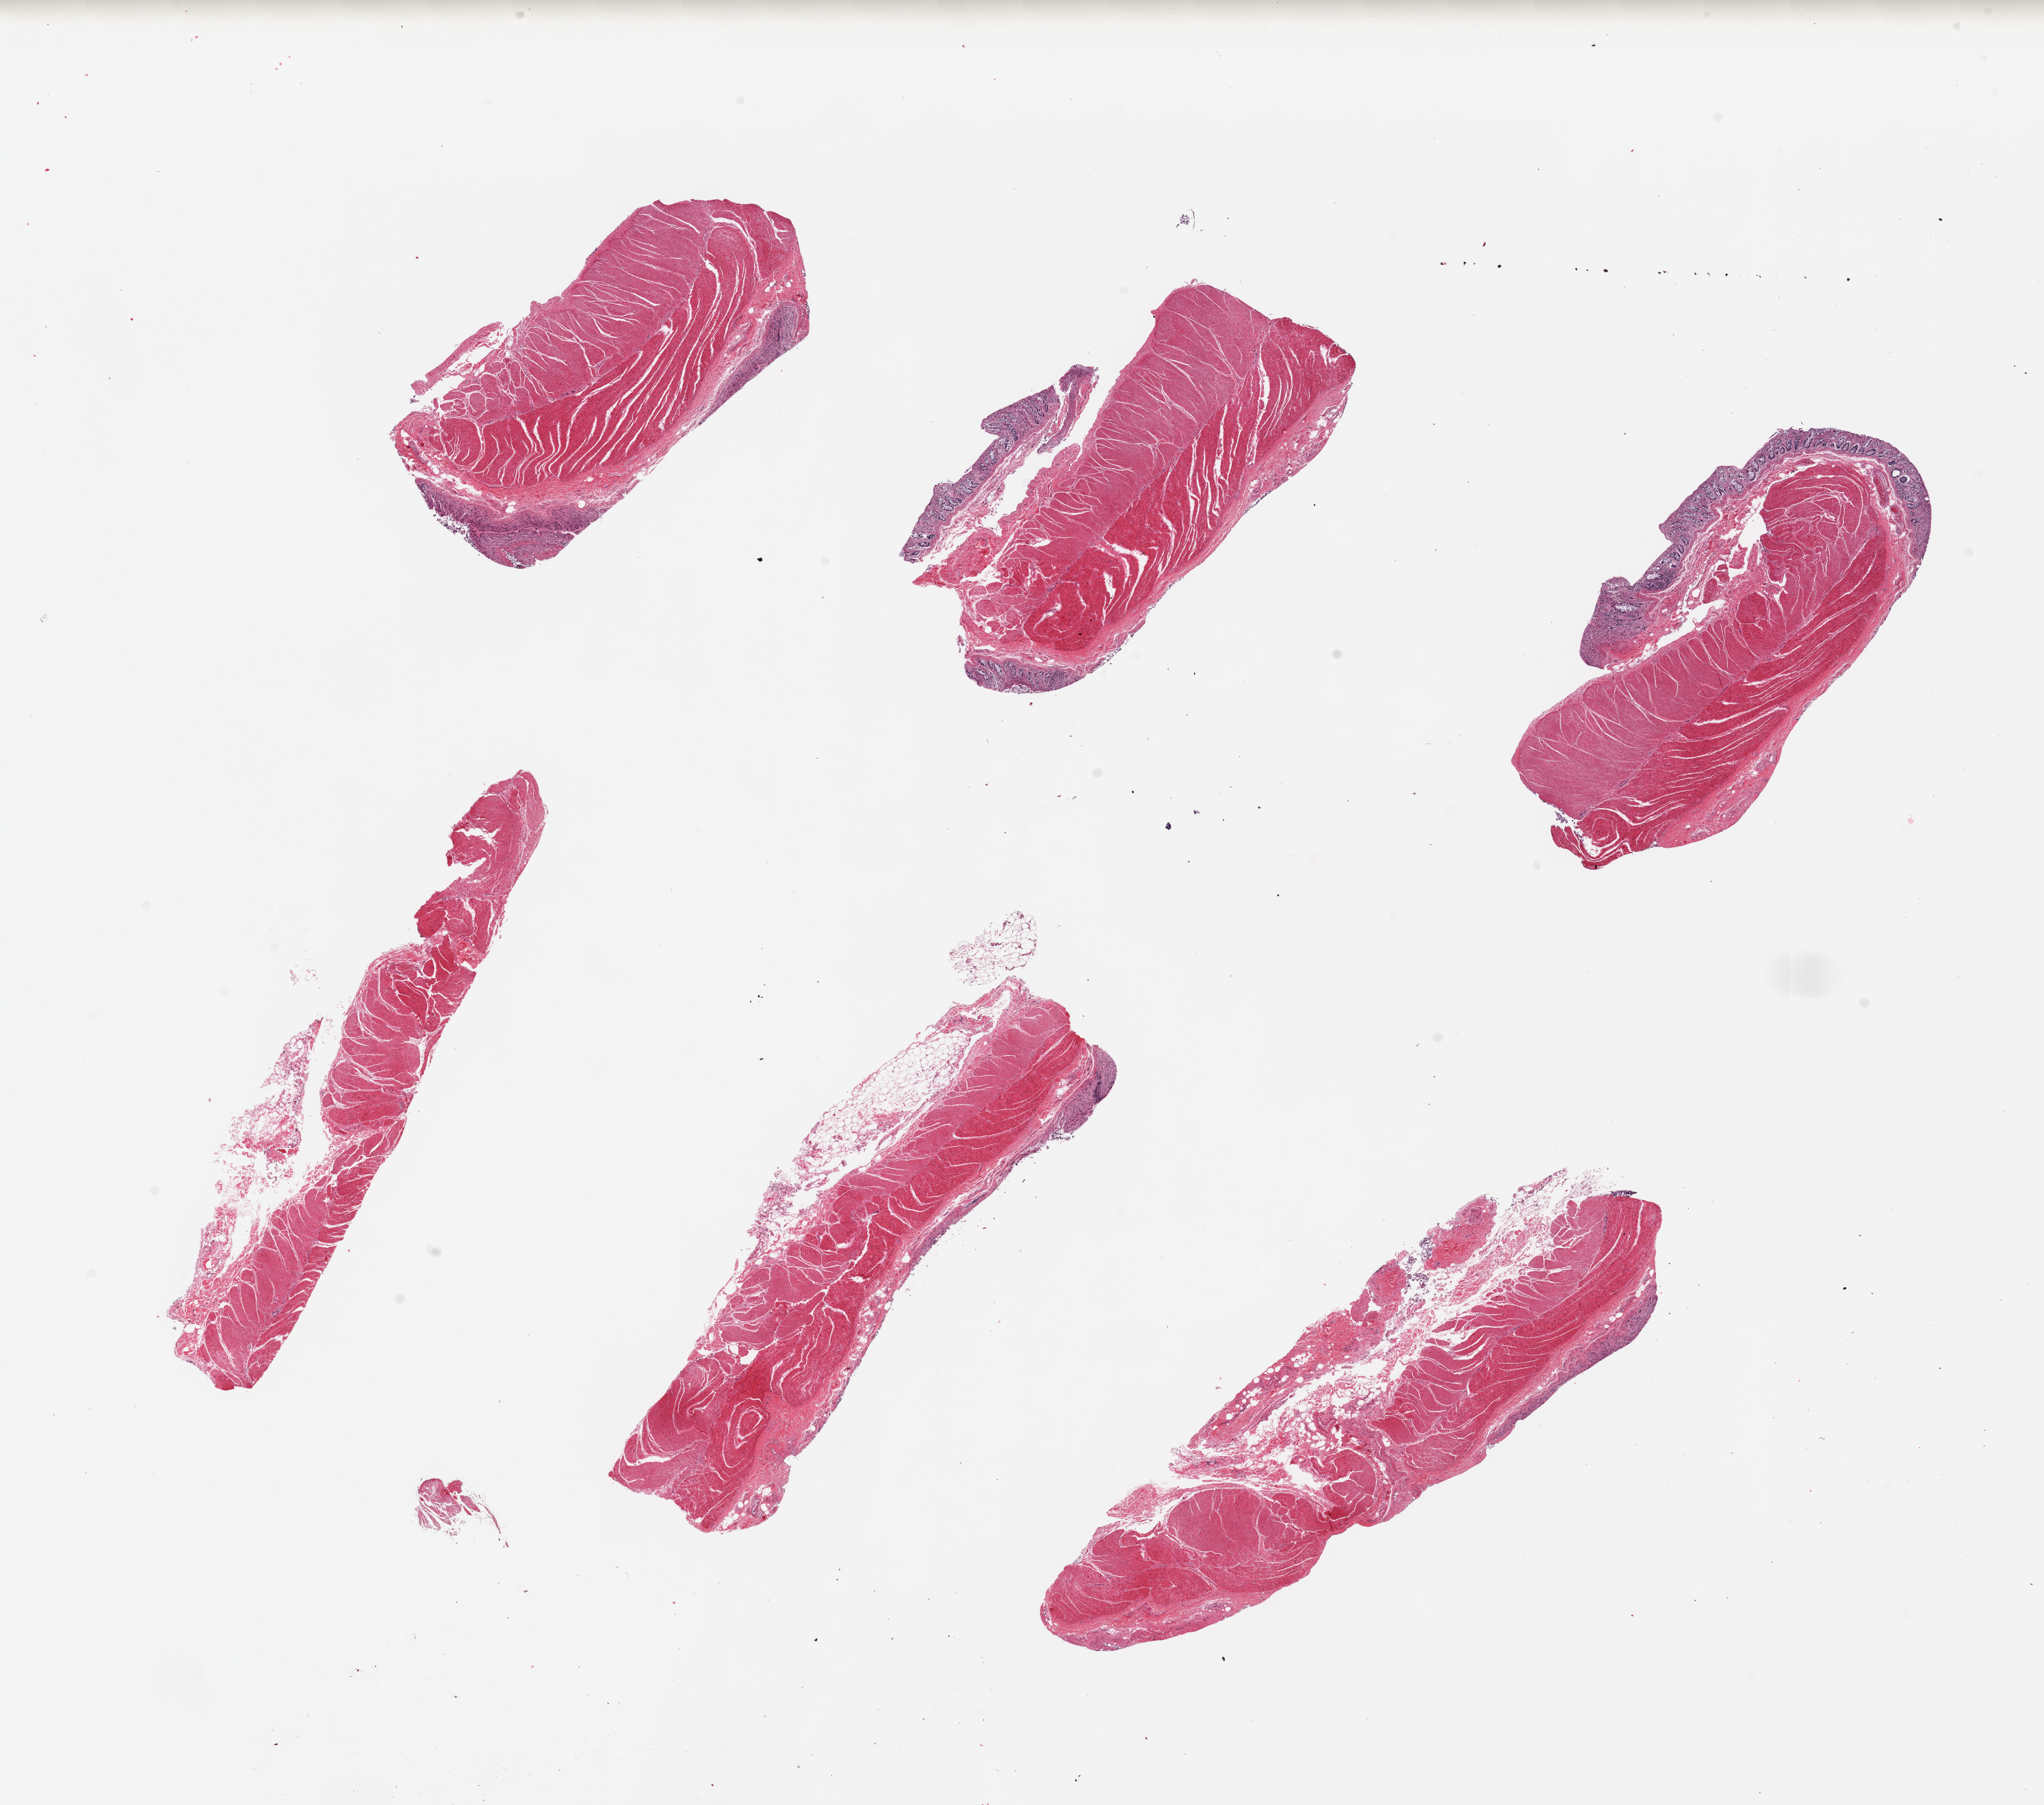
Whole-slide image, haematoxylin and eosin stain, low-resolution overview of the scanned area, about 23.6 x 20.9 mm (from a 20x scan), PAXgene-fixed, paraffin-embedded tissue, section of sigmoid colon (target tissue), tissue donor sample. Donor sex: male.
- reviewer comment on this tissue sample: 6 pieces; 5 of 6 pieces include autolyzed mucosa (not target)